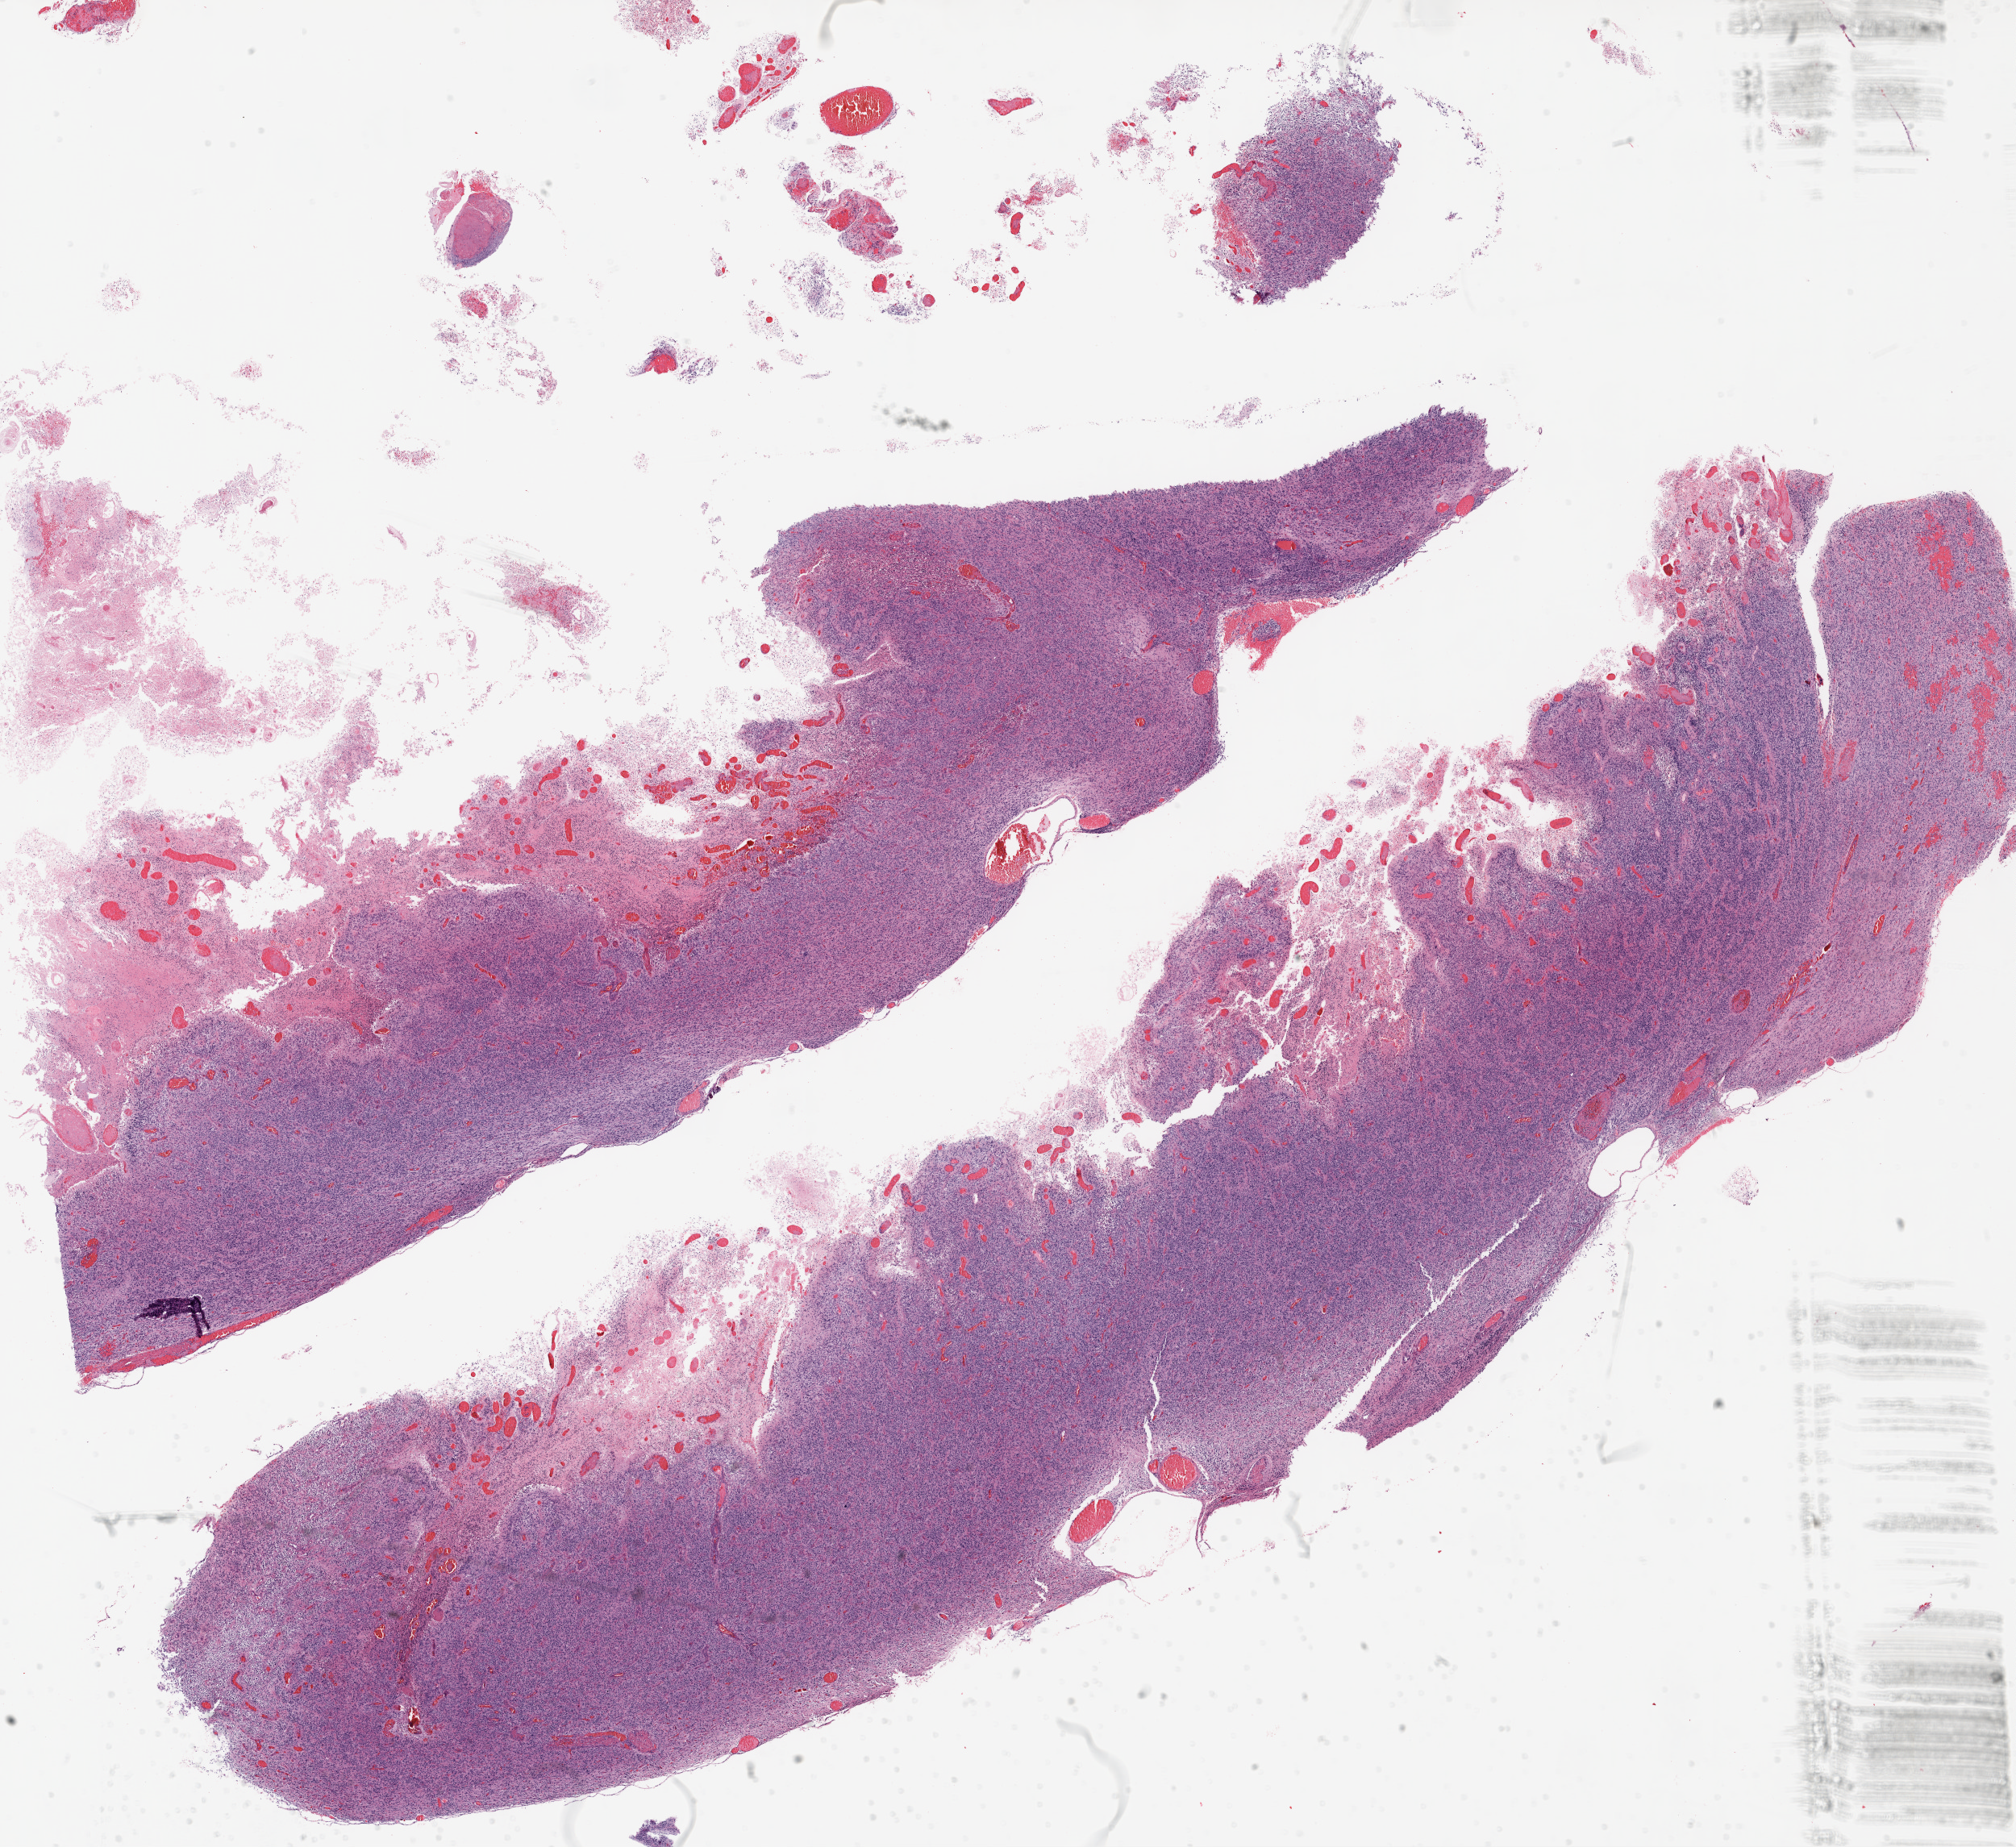
Whole-slide histology image, H&E — whole scanned area (about 20.1 x 18.4 mm) shown as a low-resolution overview; formalin-fixed paraffin-embedded (FFPE) diagnostic section; brain, primary tumour sample. Patient: male, age at initial diagnosis 39 years.
Diagnosis: Glioblastoma.